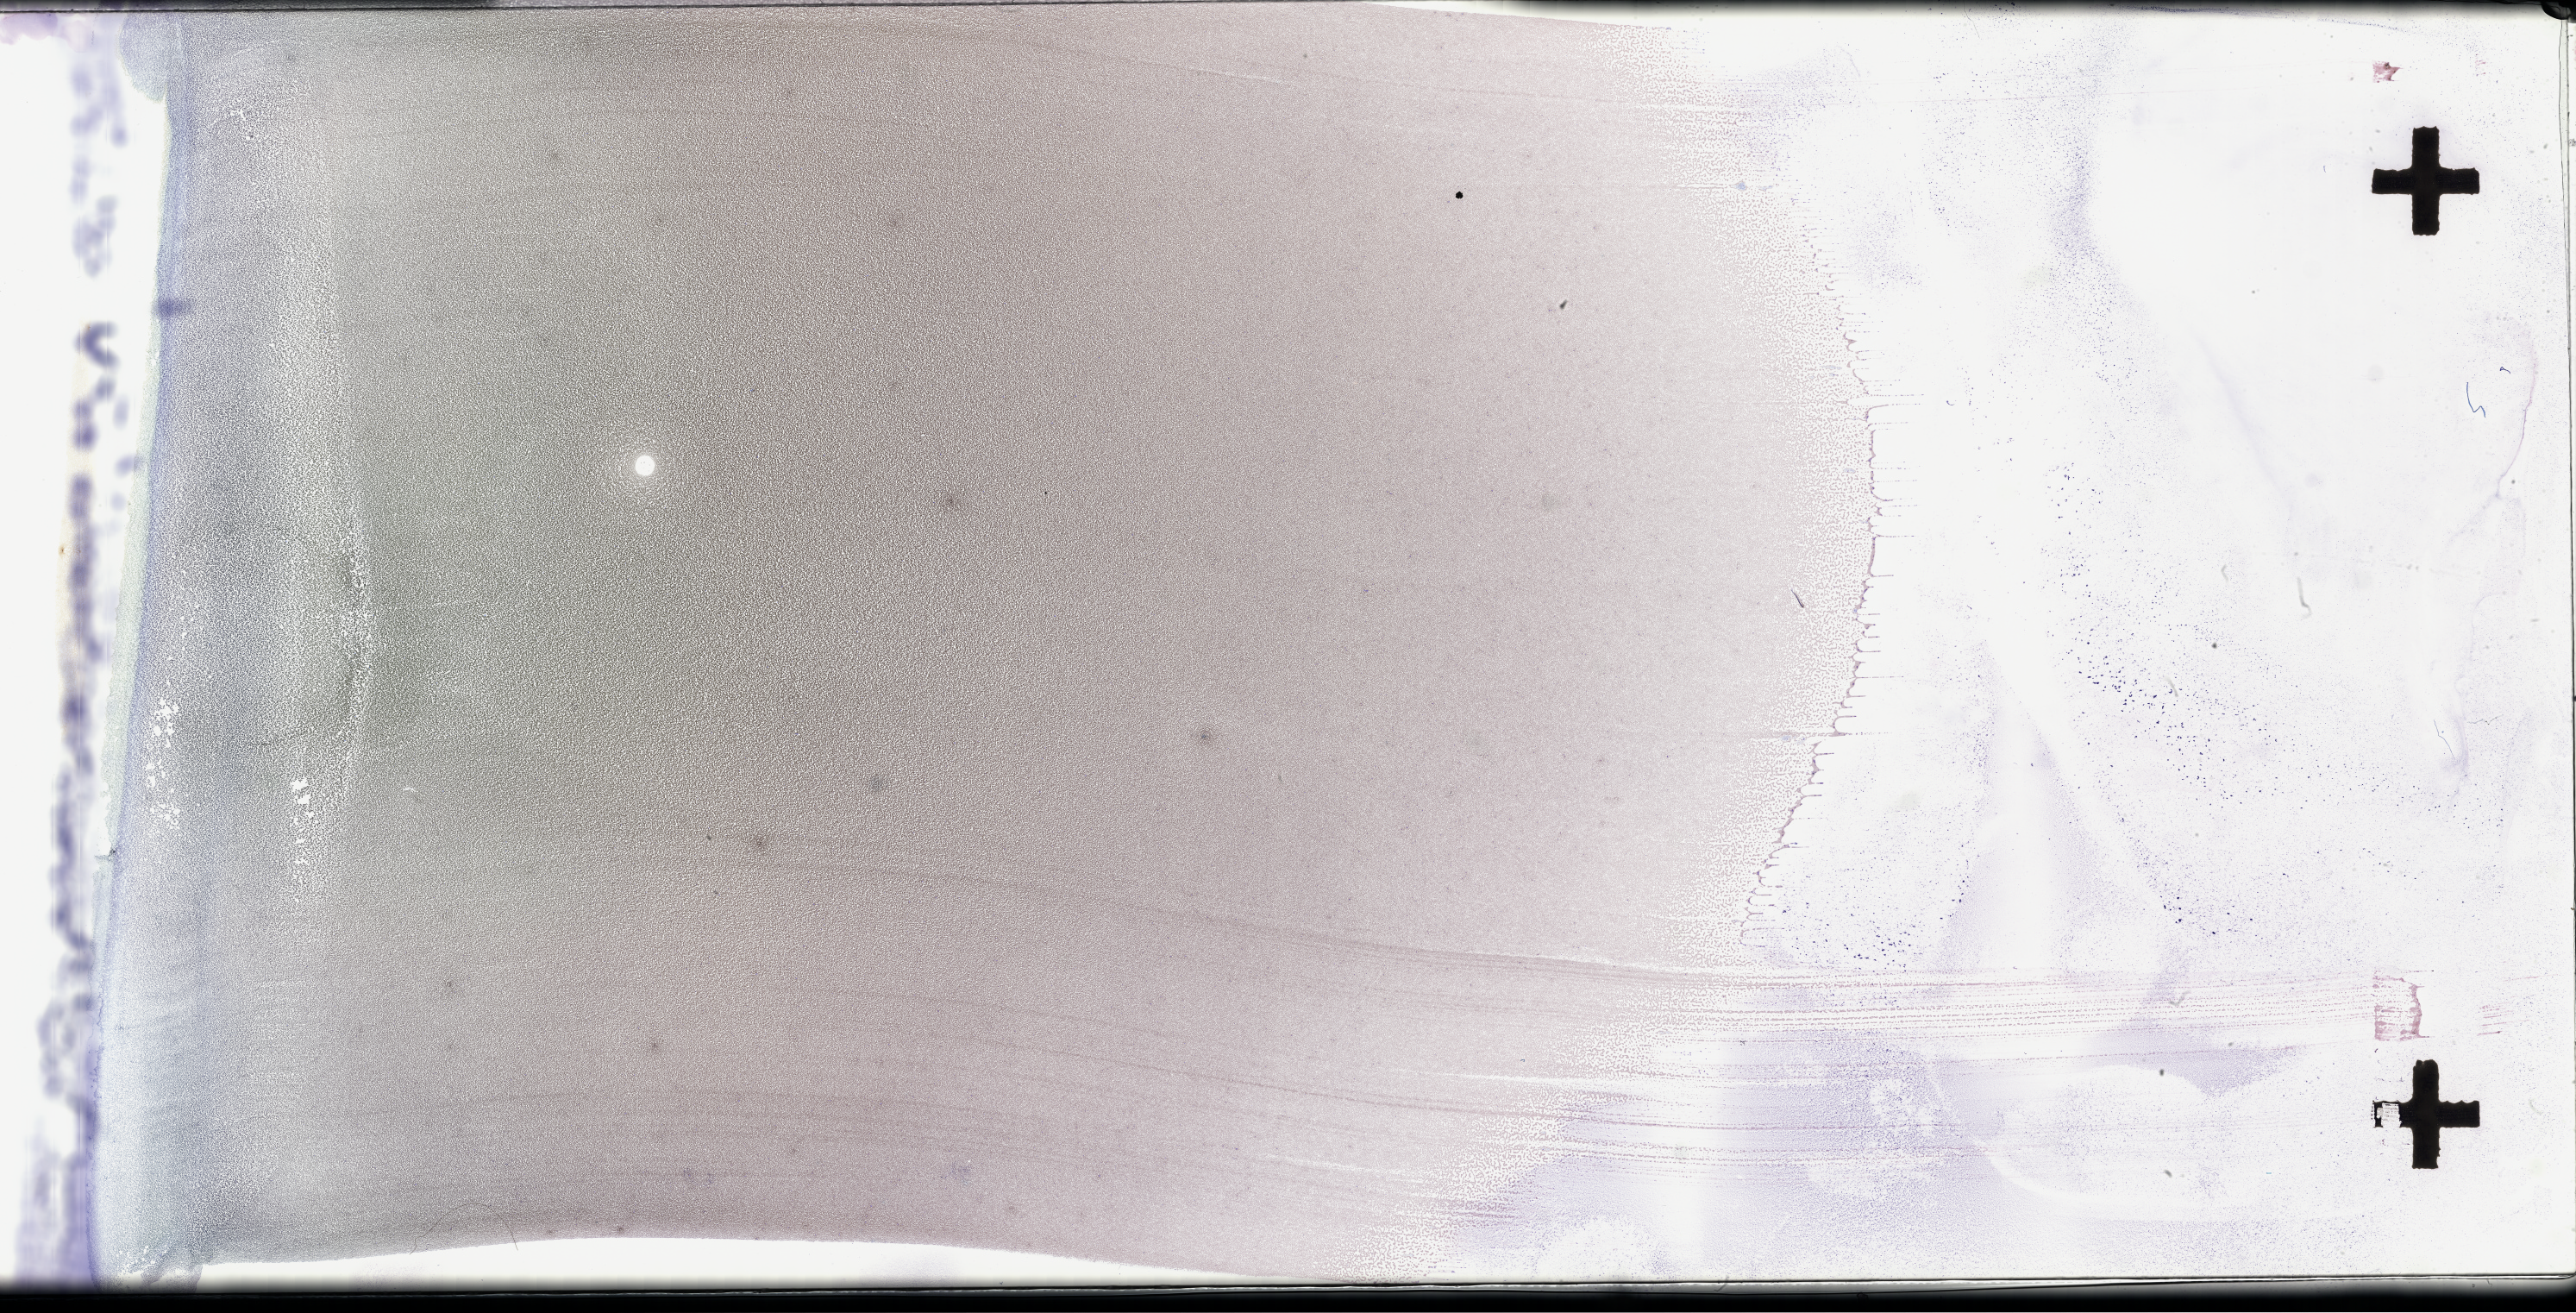
Whole-slide image of a whole blood smear, Wright-Giemsa stain — whole scanned area (about 48.2 x 24.6 mm) shown as a low-resolution overview, EDTA-anticoagulated smear, collected on treatment. Male patient.
• patient diagnosis: Plasma Cell Myeloma